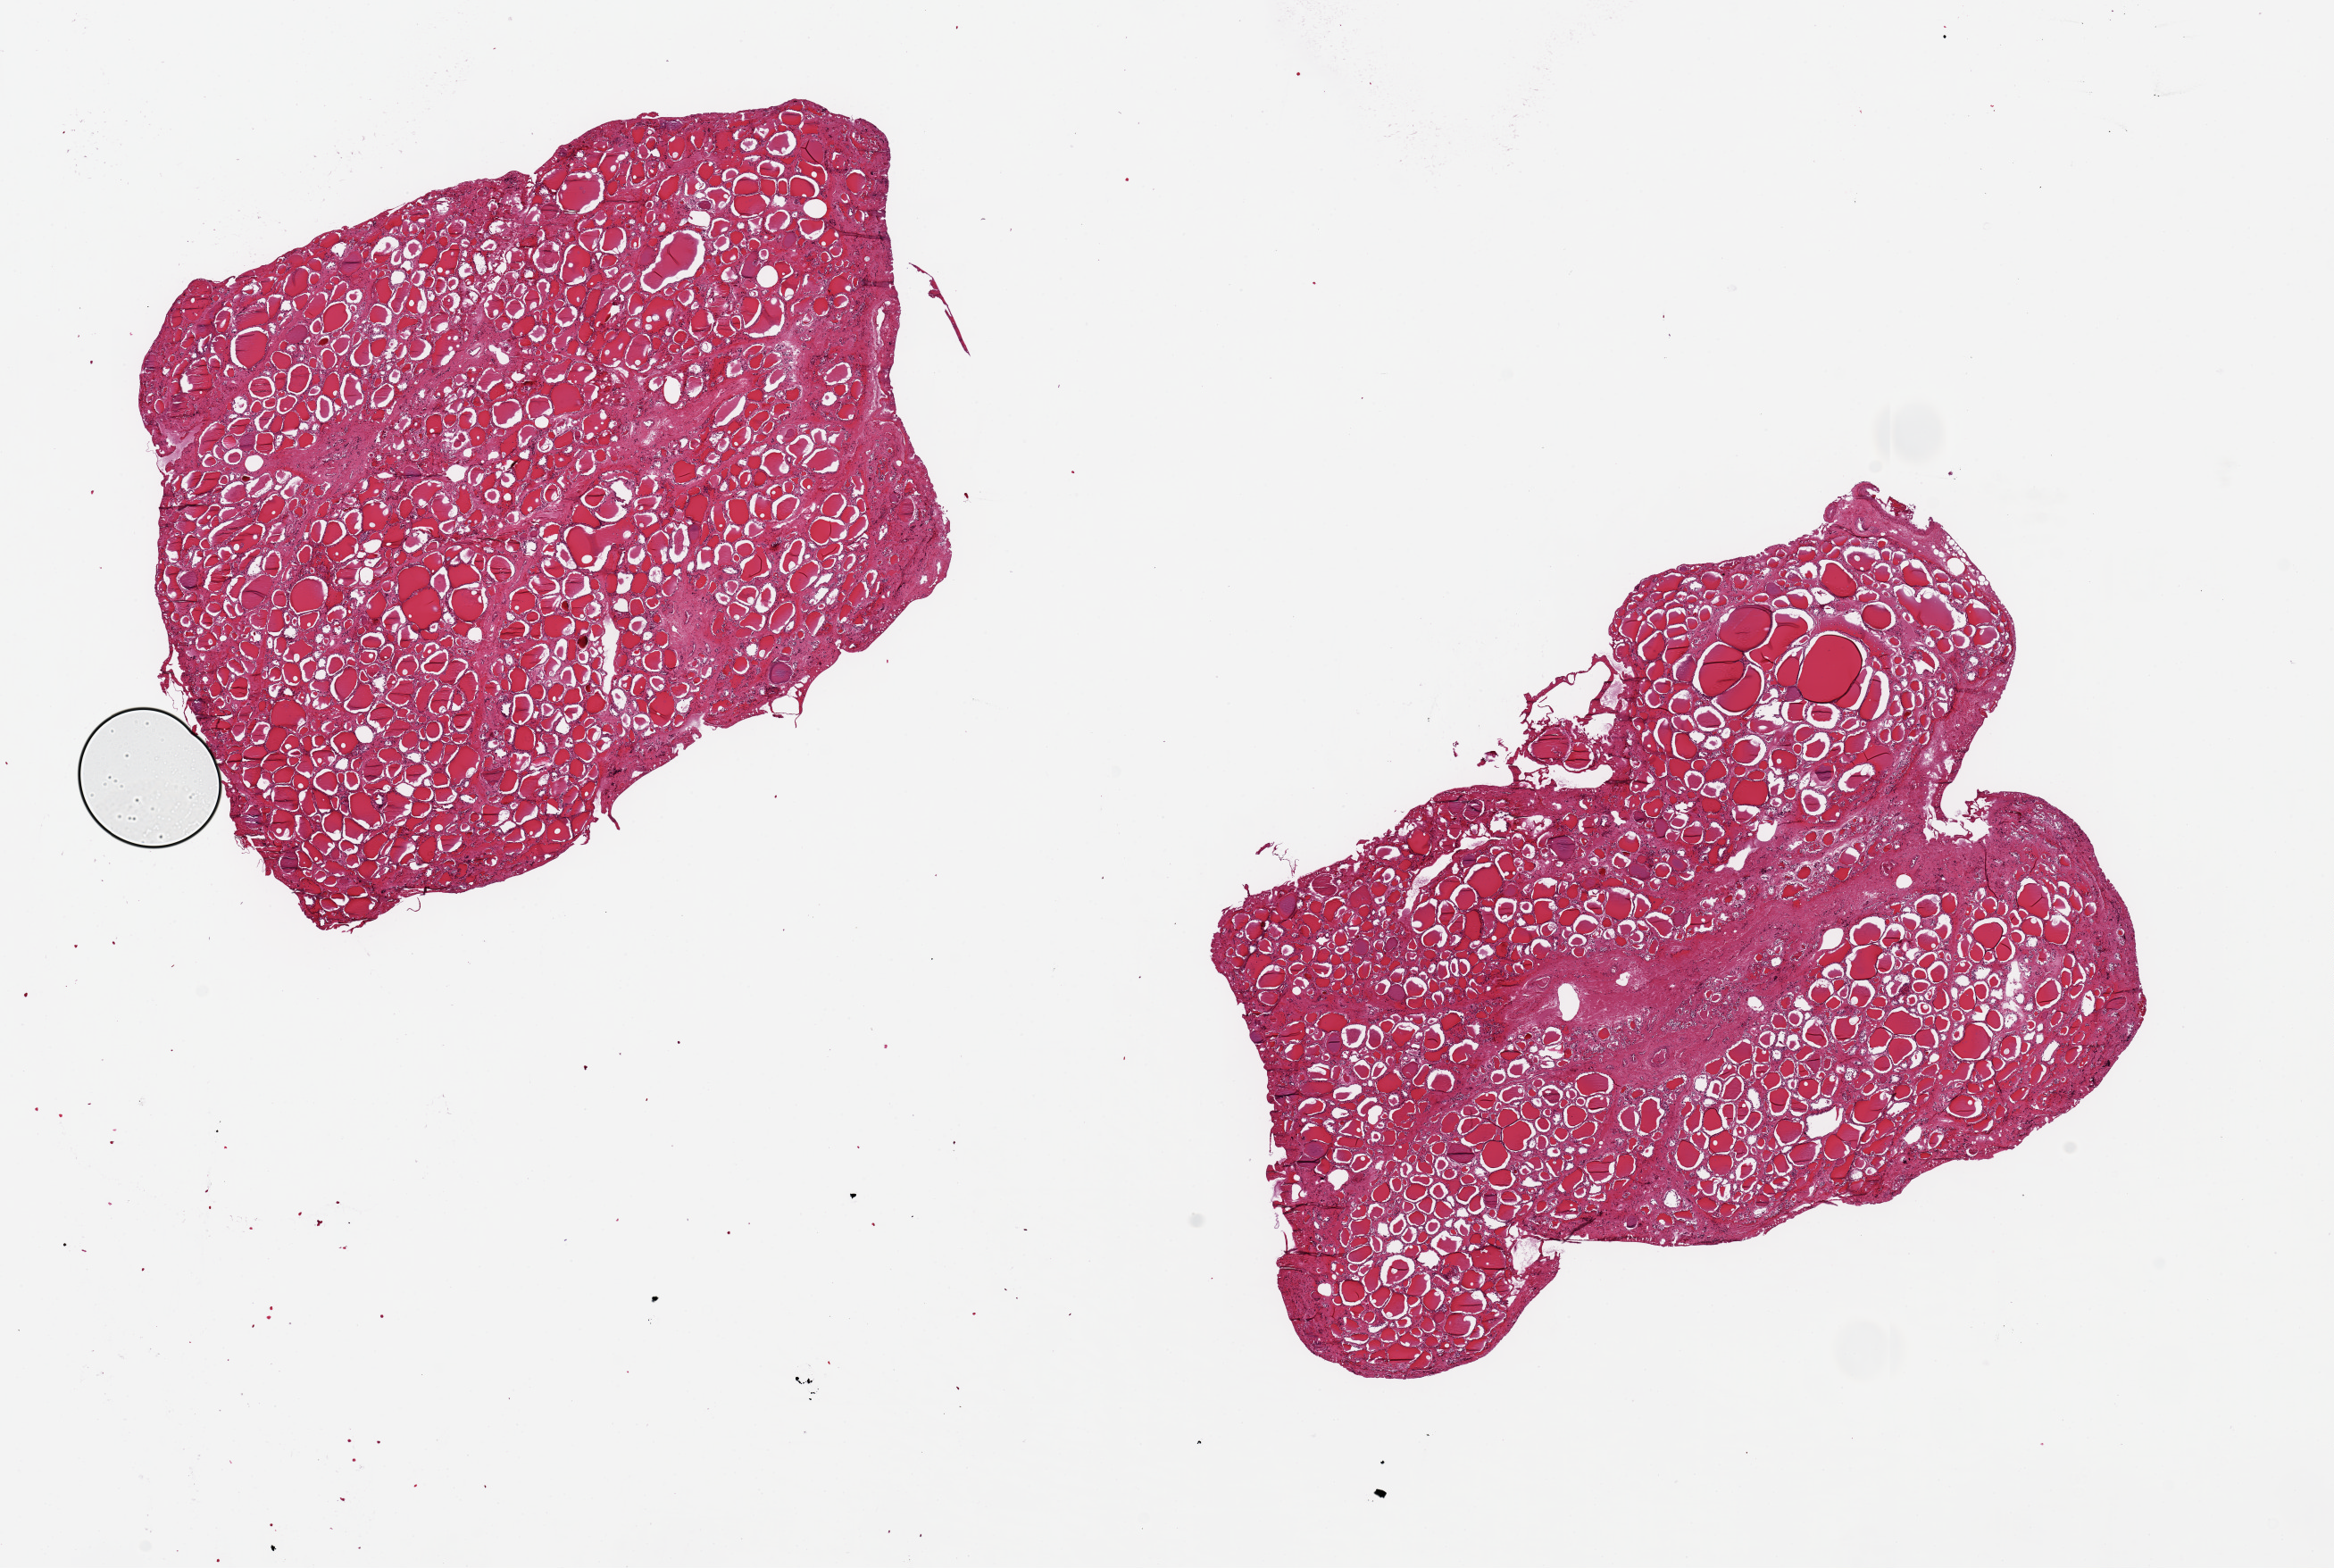
Whole-slide image, H&E stain — whole scanned area (about 20.7 x 13.9 mm) shown as a low-resolution overview. PAXgene-fixed paraffin-embedded (PFPE) section. Section of thyroid (target tissue). Donor tissue sample. Male donor.
Reviewer comment on this tissue sample: 2 pieces, 7x6 & 9x6mm; Foci of fibrosis.